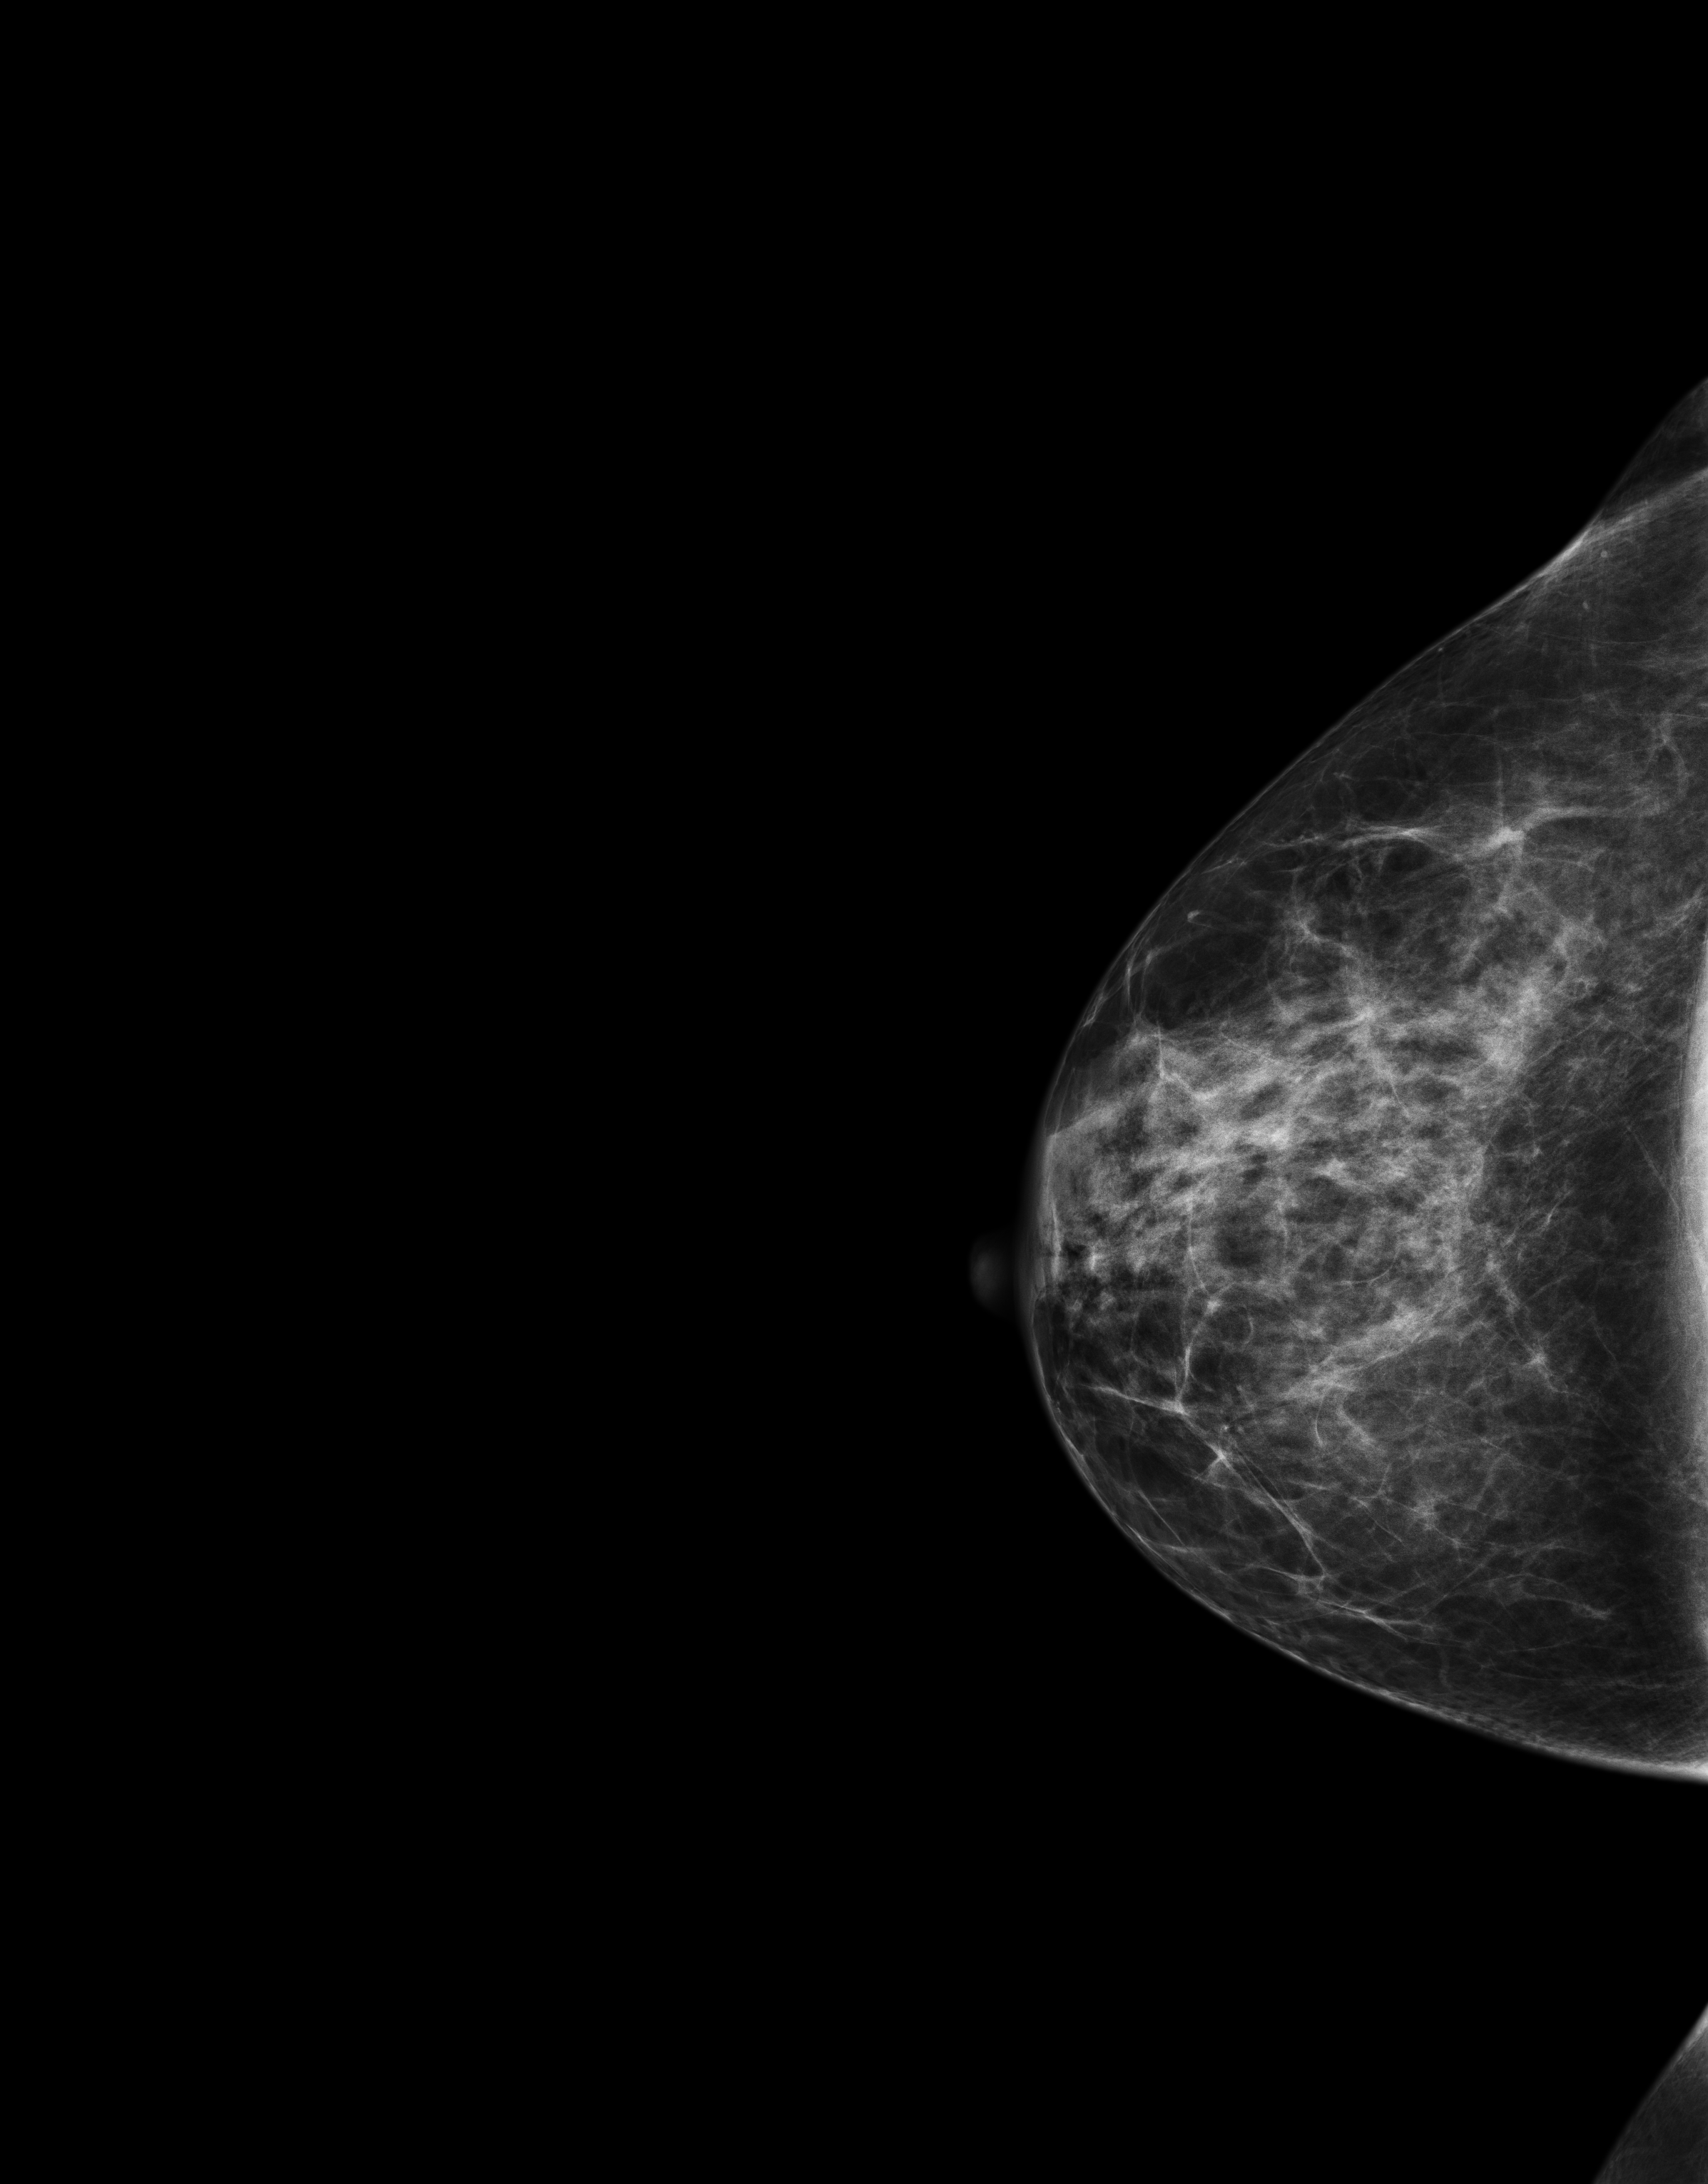
Digital mammogram (FFDM), right breast, CC view, screening examination, compressed breast thickness 64 mm. Female patient, age 56 years.
Breast density at the screening exam (both breasts): heterogeneously dense (BI-RADS density category c). Final BI-RADS category for the screening round (tomosynthesis exam, both breasts): category 1. Recall: no recall after this screen.